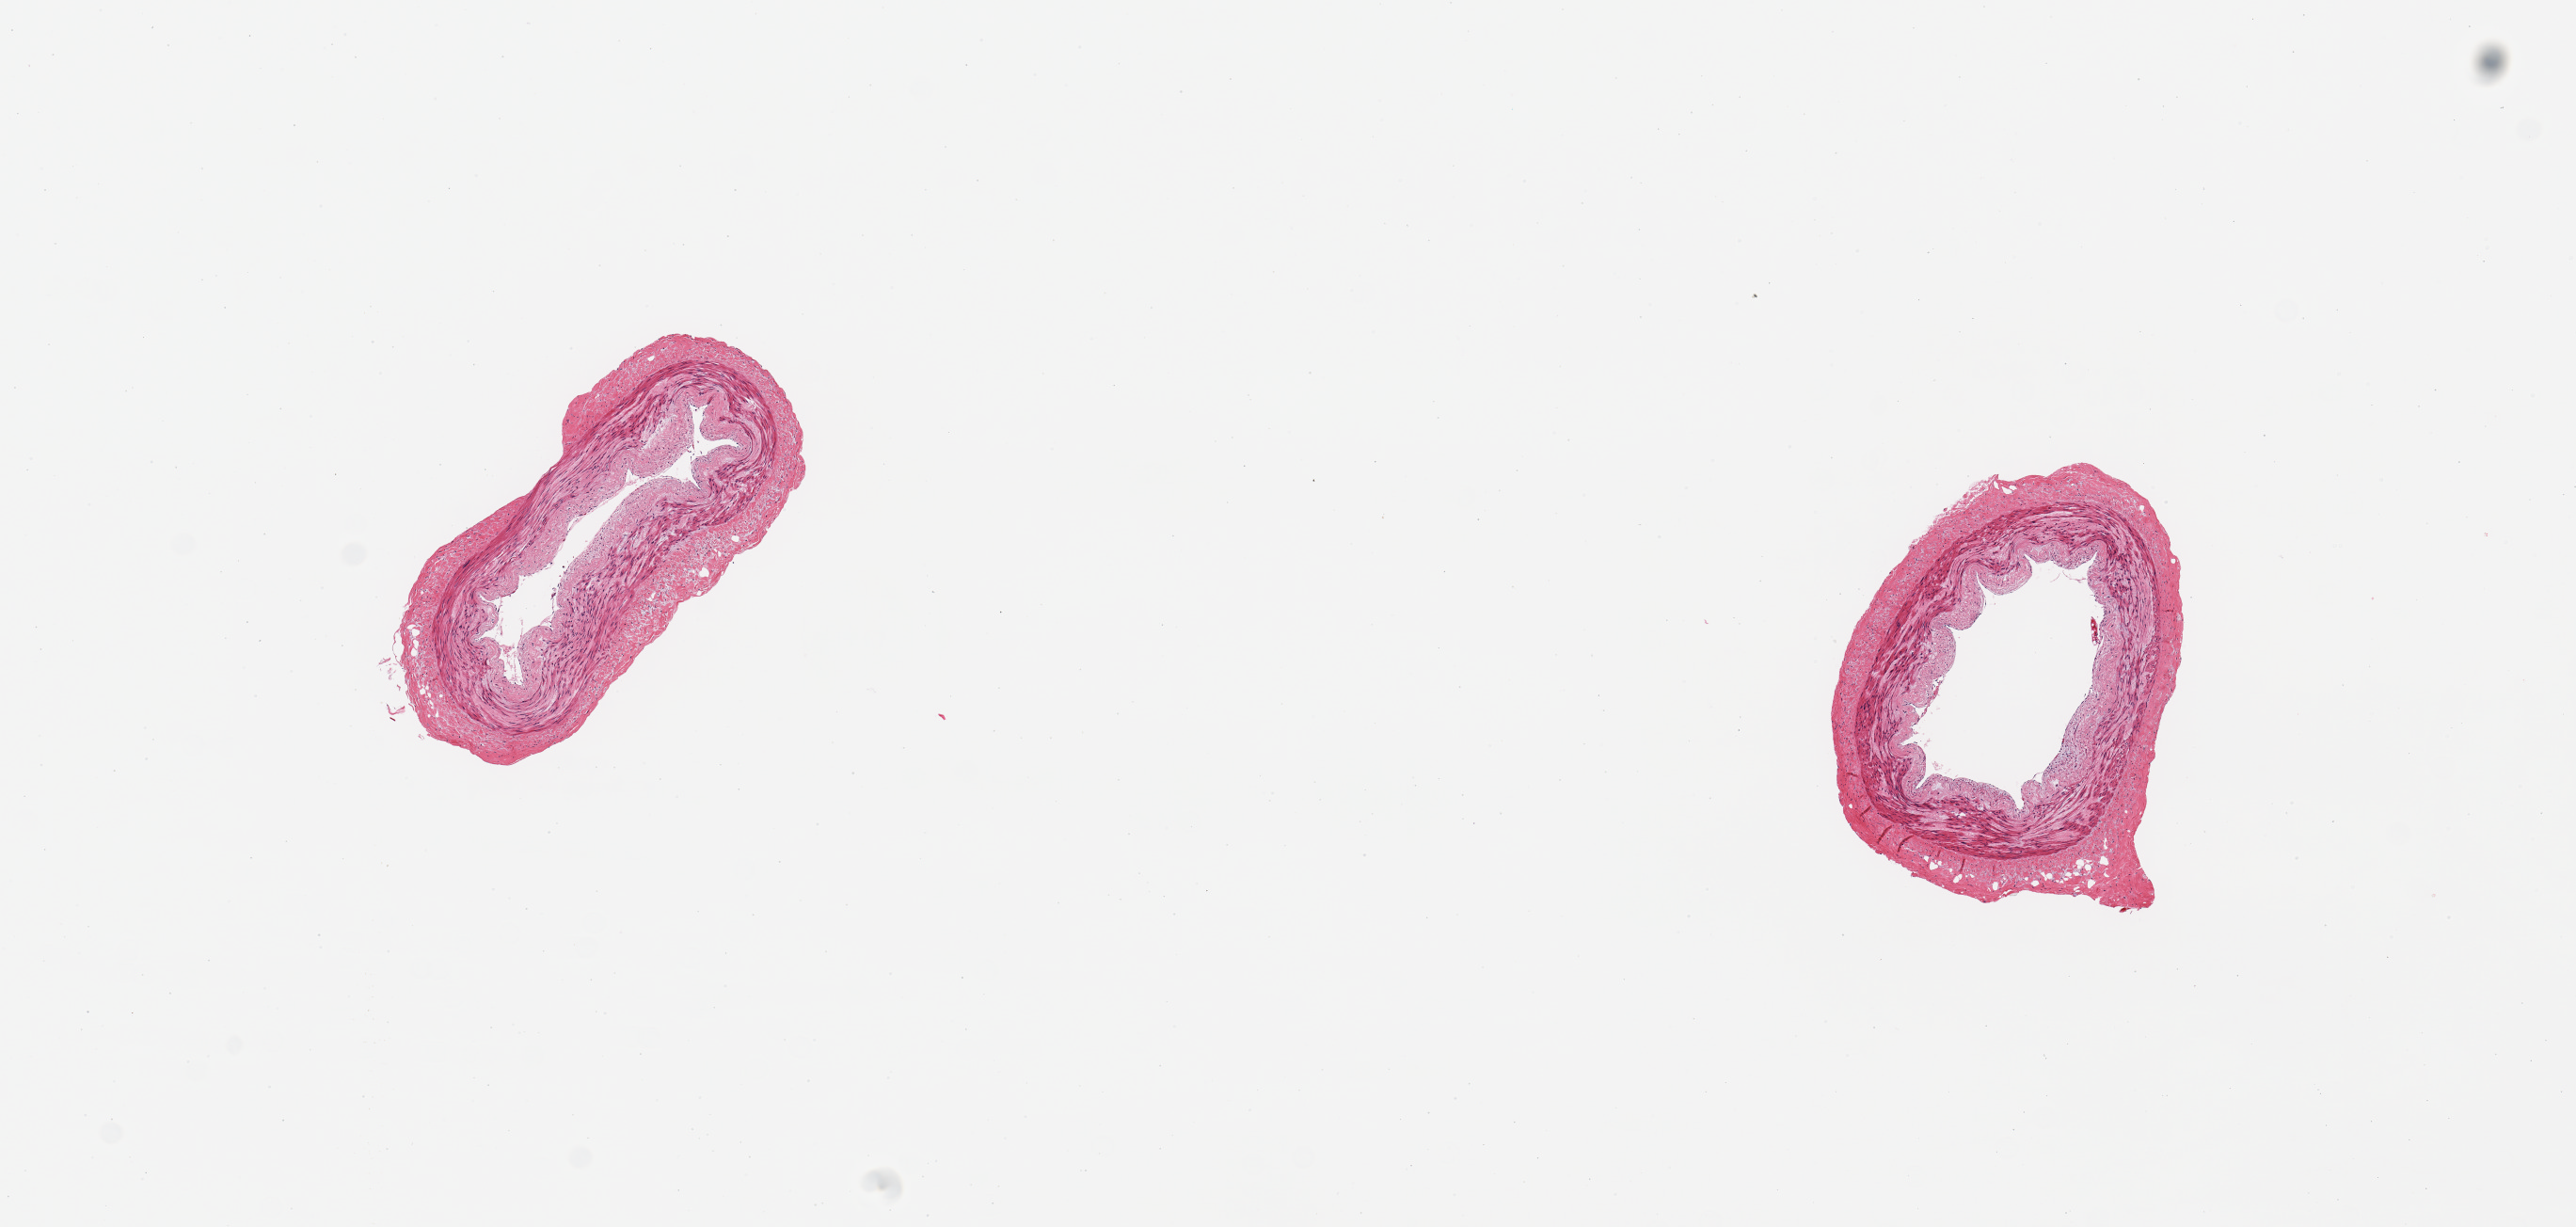
Haematoxylin and eosin whole-slide image, low-resolution overview of the scanned area, about 10.8 x 5.2 mm. PAXgene-fixed paraffin-embedded (PFPE) section. Sampled site (target tissue): tibial artery. Tissue donor sample. Donor sex: female.
Review note (as recorded): 2 pieces, no significant atherosis or adherent fat.